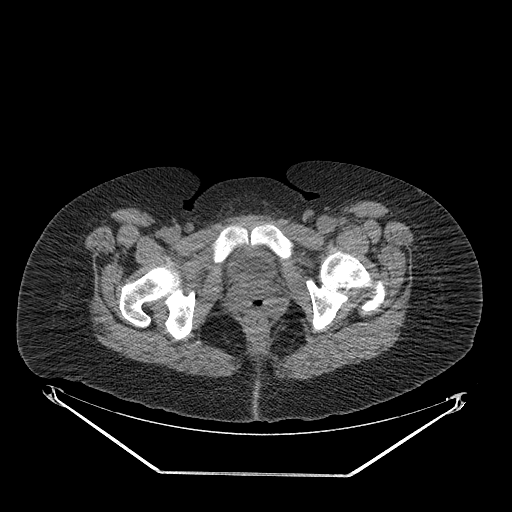
CT of an extremity soft-tissue mass (from a PET/CT study), one axial slice. Slice 55 of 267 in the series (ordered by position). Reconstruction kernel STANDARD. 140 kVp. Soft-tissue window (W 400 / L 40 HU). 3.75 mm slice thickness. 512 × 512 image matrix, field of view 500 × 500 mm. Female patient. From the clinical record (not read from this slice): histological type: myxofibrosarcoma; grade: intermediate; site of the primary tumour: left thigh.
Outlined on this slice (expert contour drawn on MRI and transferred to this co-registered scan by the dataset authors):
- gross tumour volume including surrounding oedema: bounding box <274,222,355,250> (left, top, right, bottom; pixels)